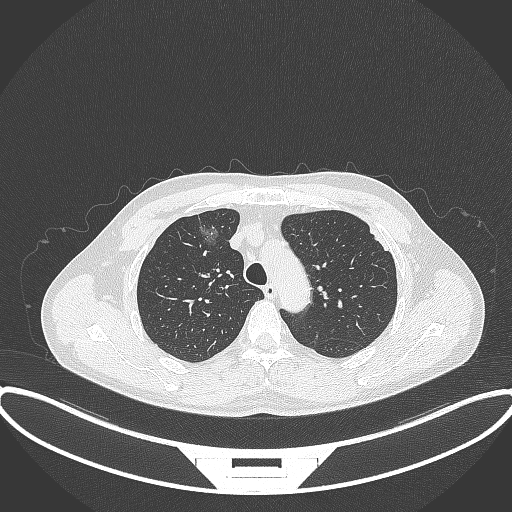
Chest CT, one axial slice; slice 276 of 395 in the series (ordered by position); reconstruction kernel B70f; 120 kVp; lung window (W 1500 / L -600 HU); 1 mm slice thickness; 512 × 512 image matrix, field of view 424 × 424 mm. Male patient, age 60 years. From the clinical record (not read from this slice): clinical TNM (as recorded): T1c N0 M0.
Outlined on this slice (rectangle marked by the reading radiologist):
- lung tumour (recorded histology: adenocarcinoma): bounding box [x1, y1, x2, y2] px = [196, 216, 226, 255]